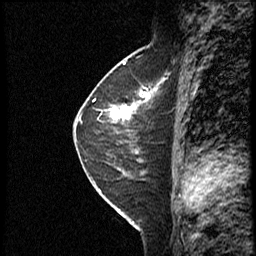
Breast MRI (dynamic contrast-enhanced), one sagittal slice. Position 21 of 40 along the scan axis. Dynamic contrast-enhanced study with each time point stored as its own series, time point 2 of 4 at this slice position (early post-contrast, ordered by acquisition time). 1.5 T. TE 4.2 ms, TR 18.8 ms. 3 mm slice thickness. 256 × 256 image matrix, field of view 200 × 200 mm. Female patient. Case-level facts recorded for this patient, not image findings: setting: breast cancer imaged before/during neoadjuvant chemotherapy; receptor status: HER2-positive.
Structures marked on this image (semi-automatic segmentation, software-assisted and operator-edited):
- analysis volume of interest (the breast-tissue region the enhancement analysis was run in; not a lesion): bounding box (x1, y1, x2, y2) in pixels: (91, 79, 167, 153)
- tumour enhancement mask (voxels above the 100 % enhancement threshold inside the analysis volume of interest): (111, 87, 157, 121)